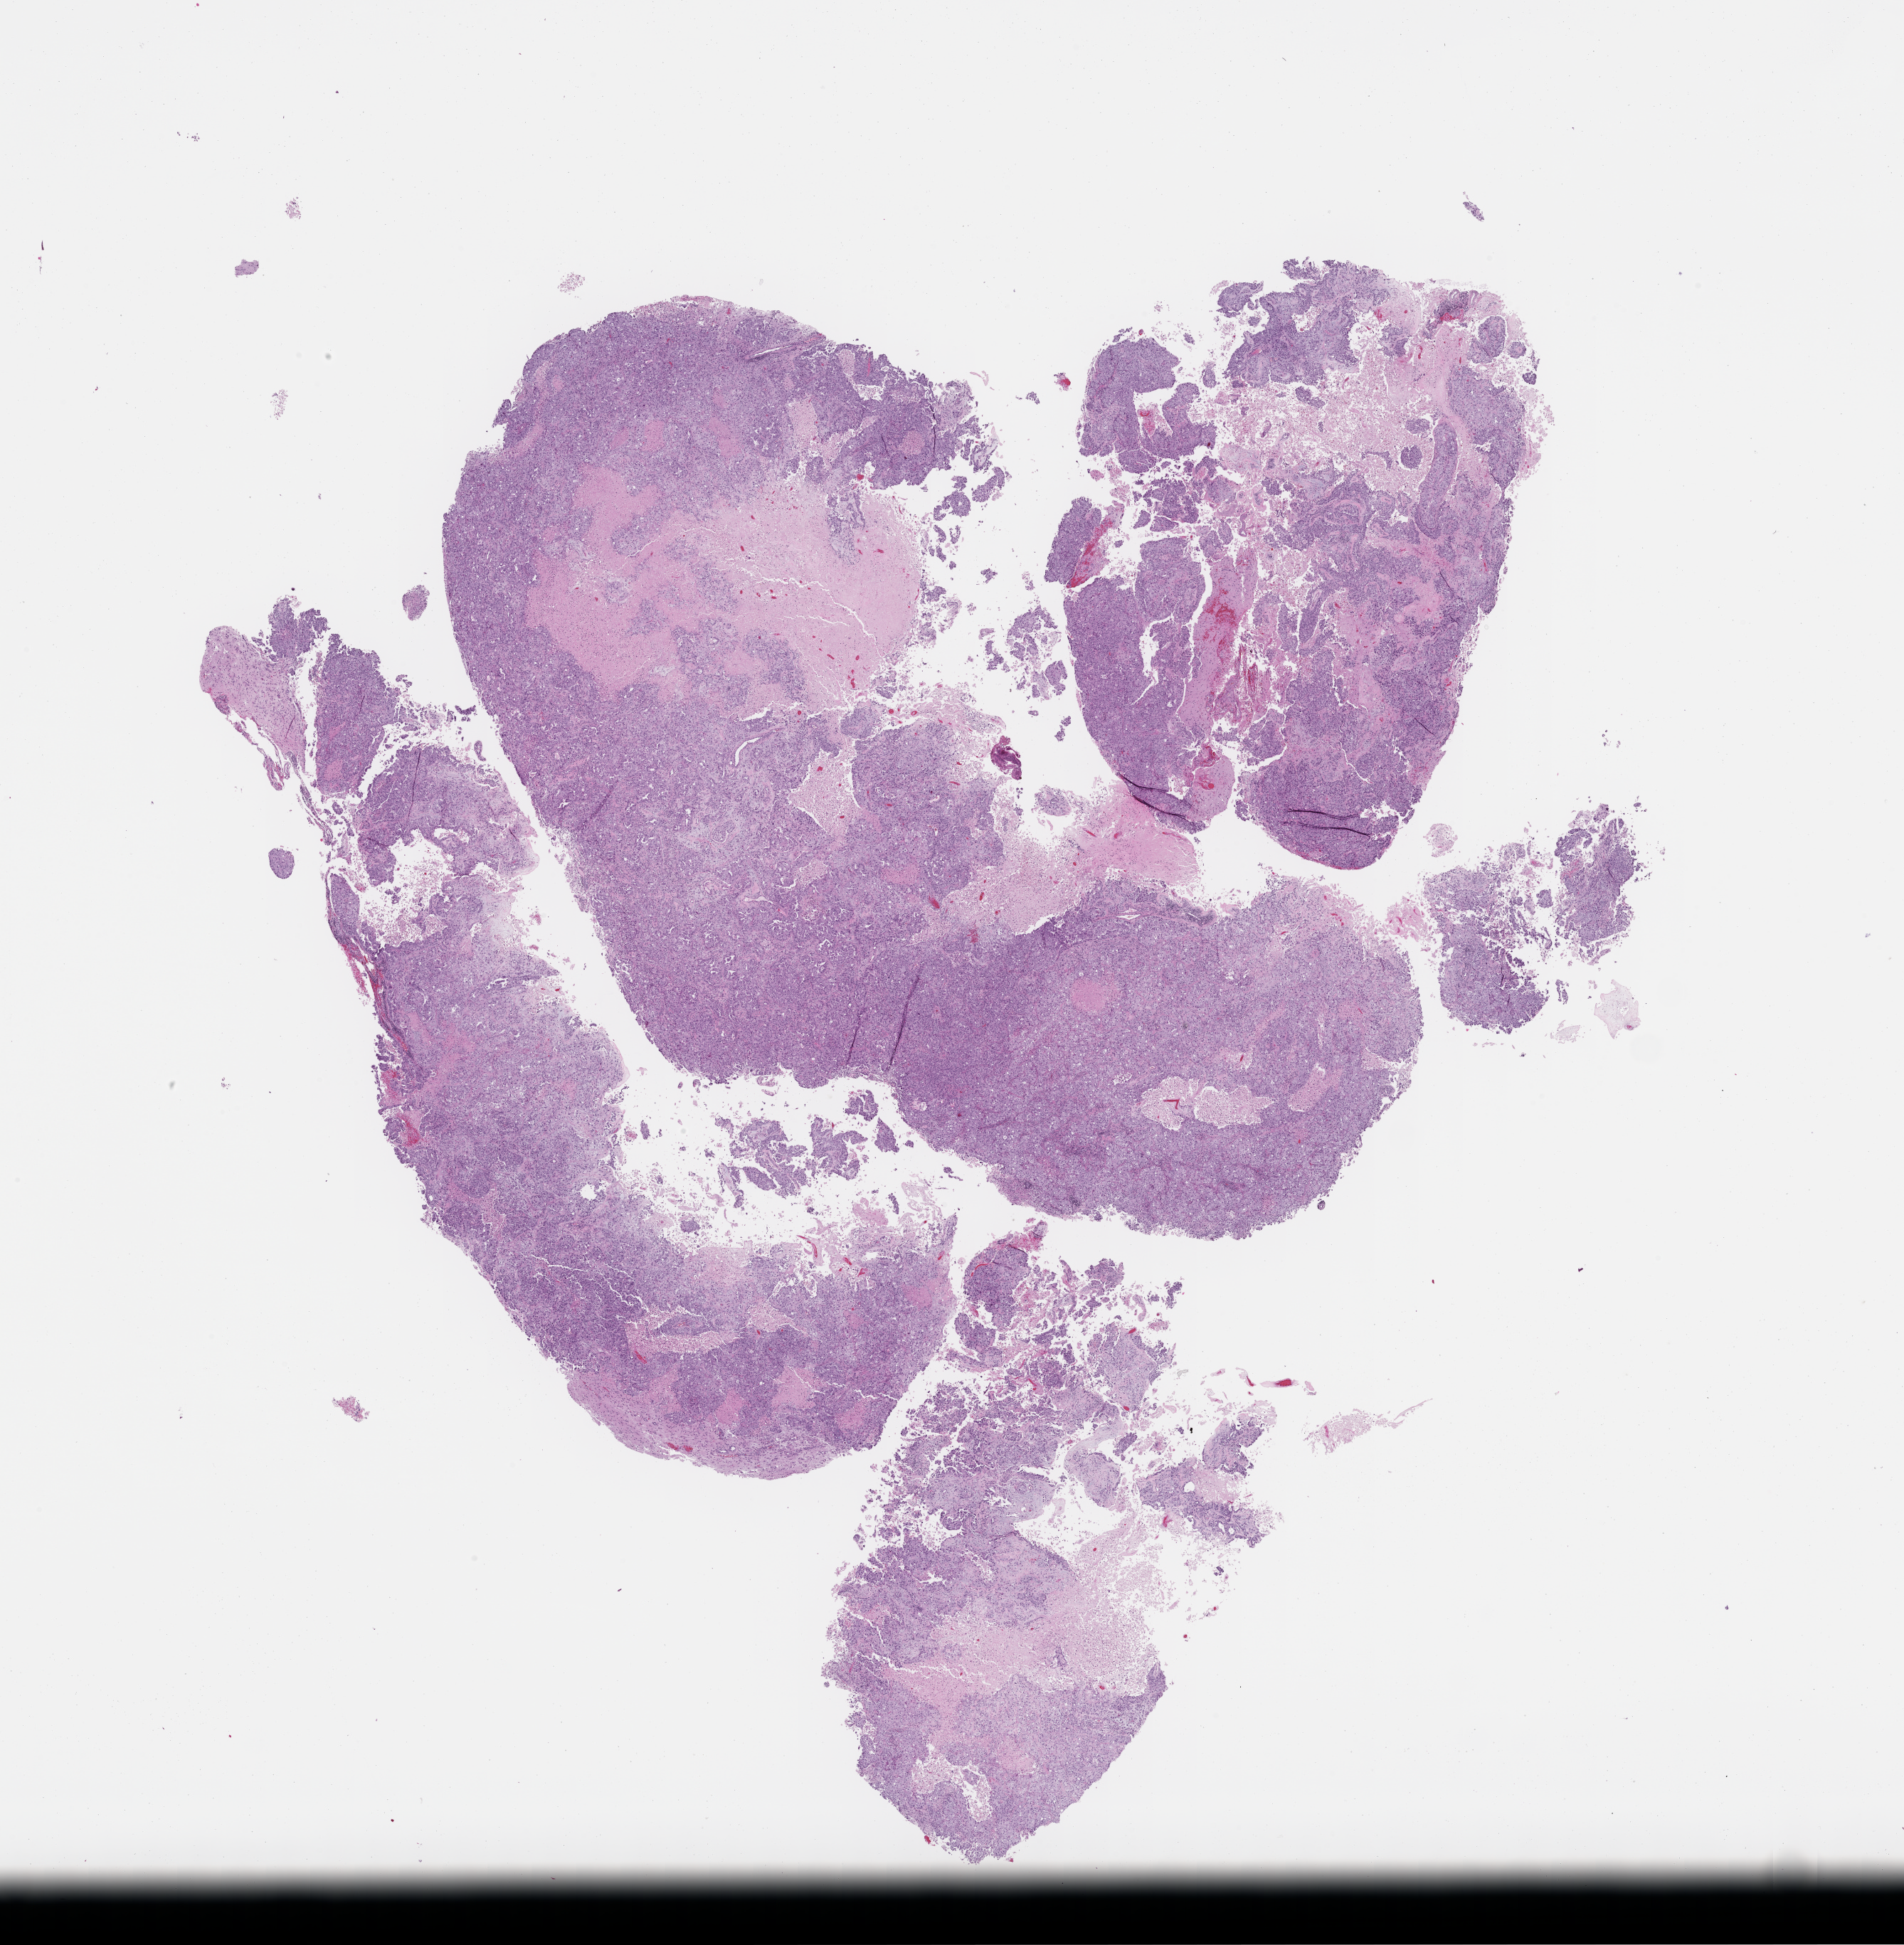
H&E whole-slide image — low-resolution overview of the scanned area, about 21.6 x 22.1 mm. FFPE section. Female patient.
This section: metastatic tumor tissue. Patient diagnosis (primary): Non-Small Cell Lung Carcinoma.